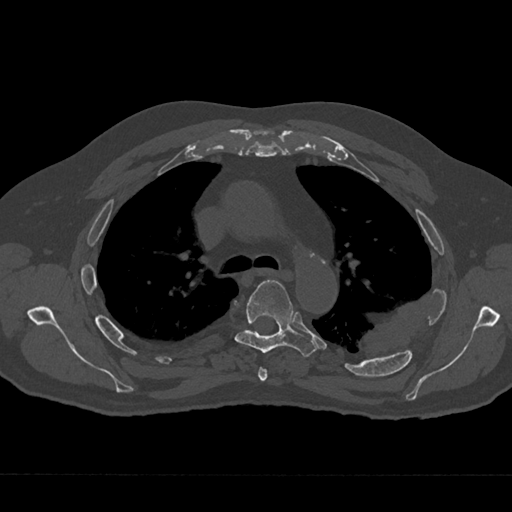
CT including the spine, one axial slice; slice 479 of 797 in the series (ordered by position); 120 kVp; bone window (W 1800 / L 400 HU); 512 × 512 image matrix, field of view 377 × 377 mm. Male patient, age 75 years. Case-level facts recorded for this patient, not image findings: primary cancer: renal; vertebrae with lytic lesions (as recorded): T4.
Outlined on this slice (semi-automatic segmentation, software-assisted and operator-edited):
- T4 vertebra: box from (x=258, y=367) to (x=268, y=382) px
- T5 vertebra: (x=235, y=280)–(x=317, y=357)